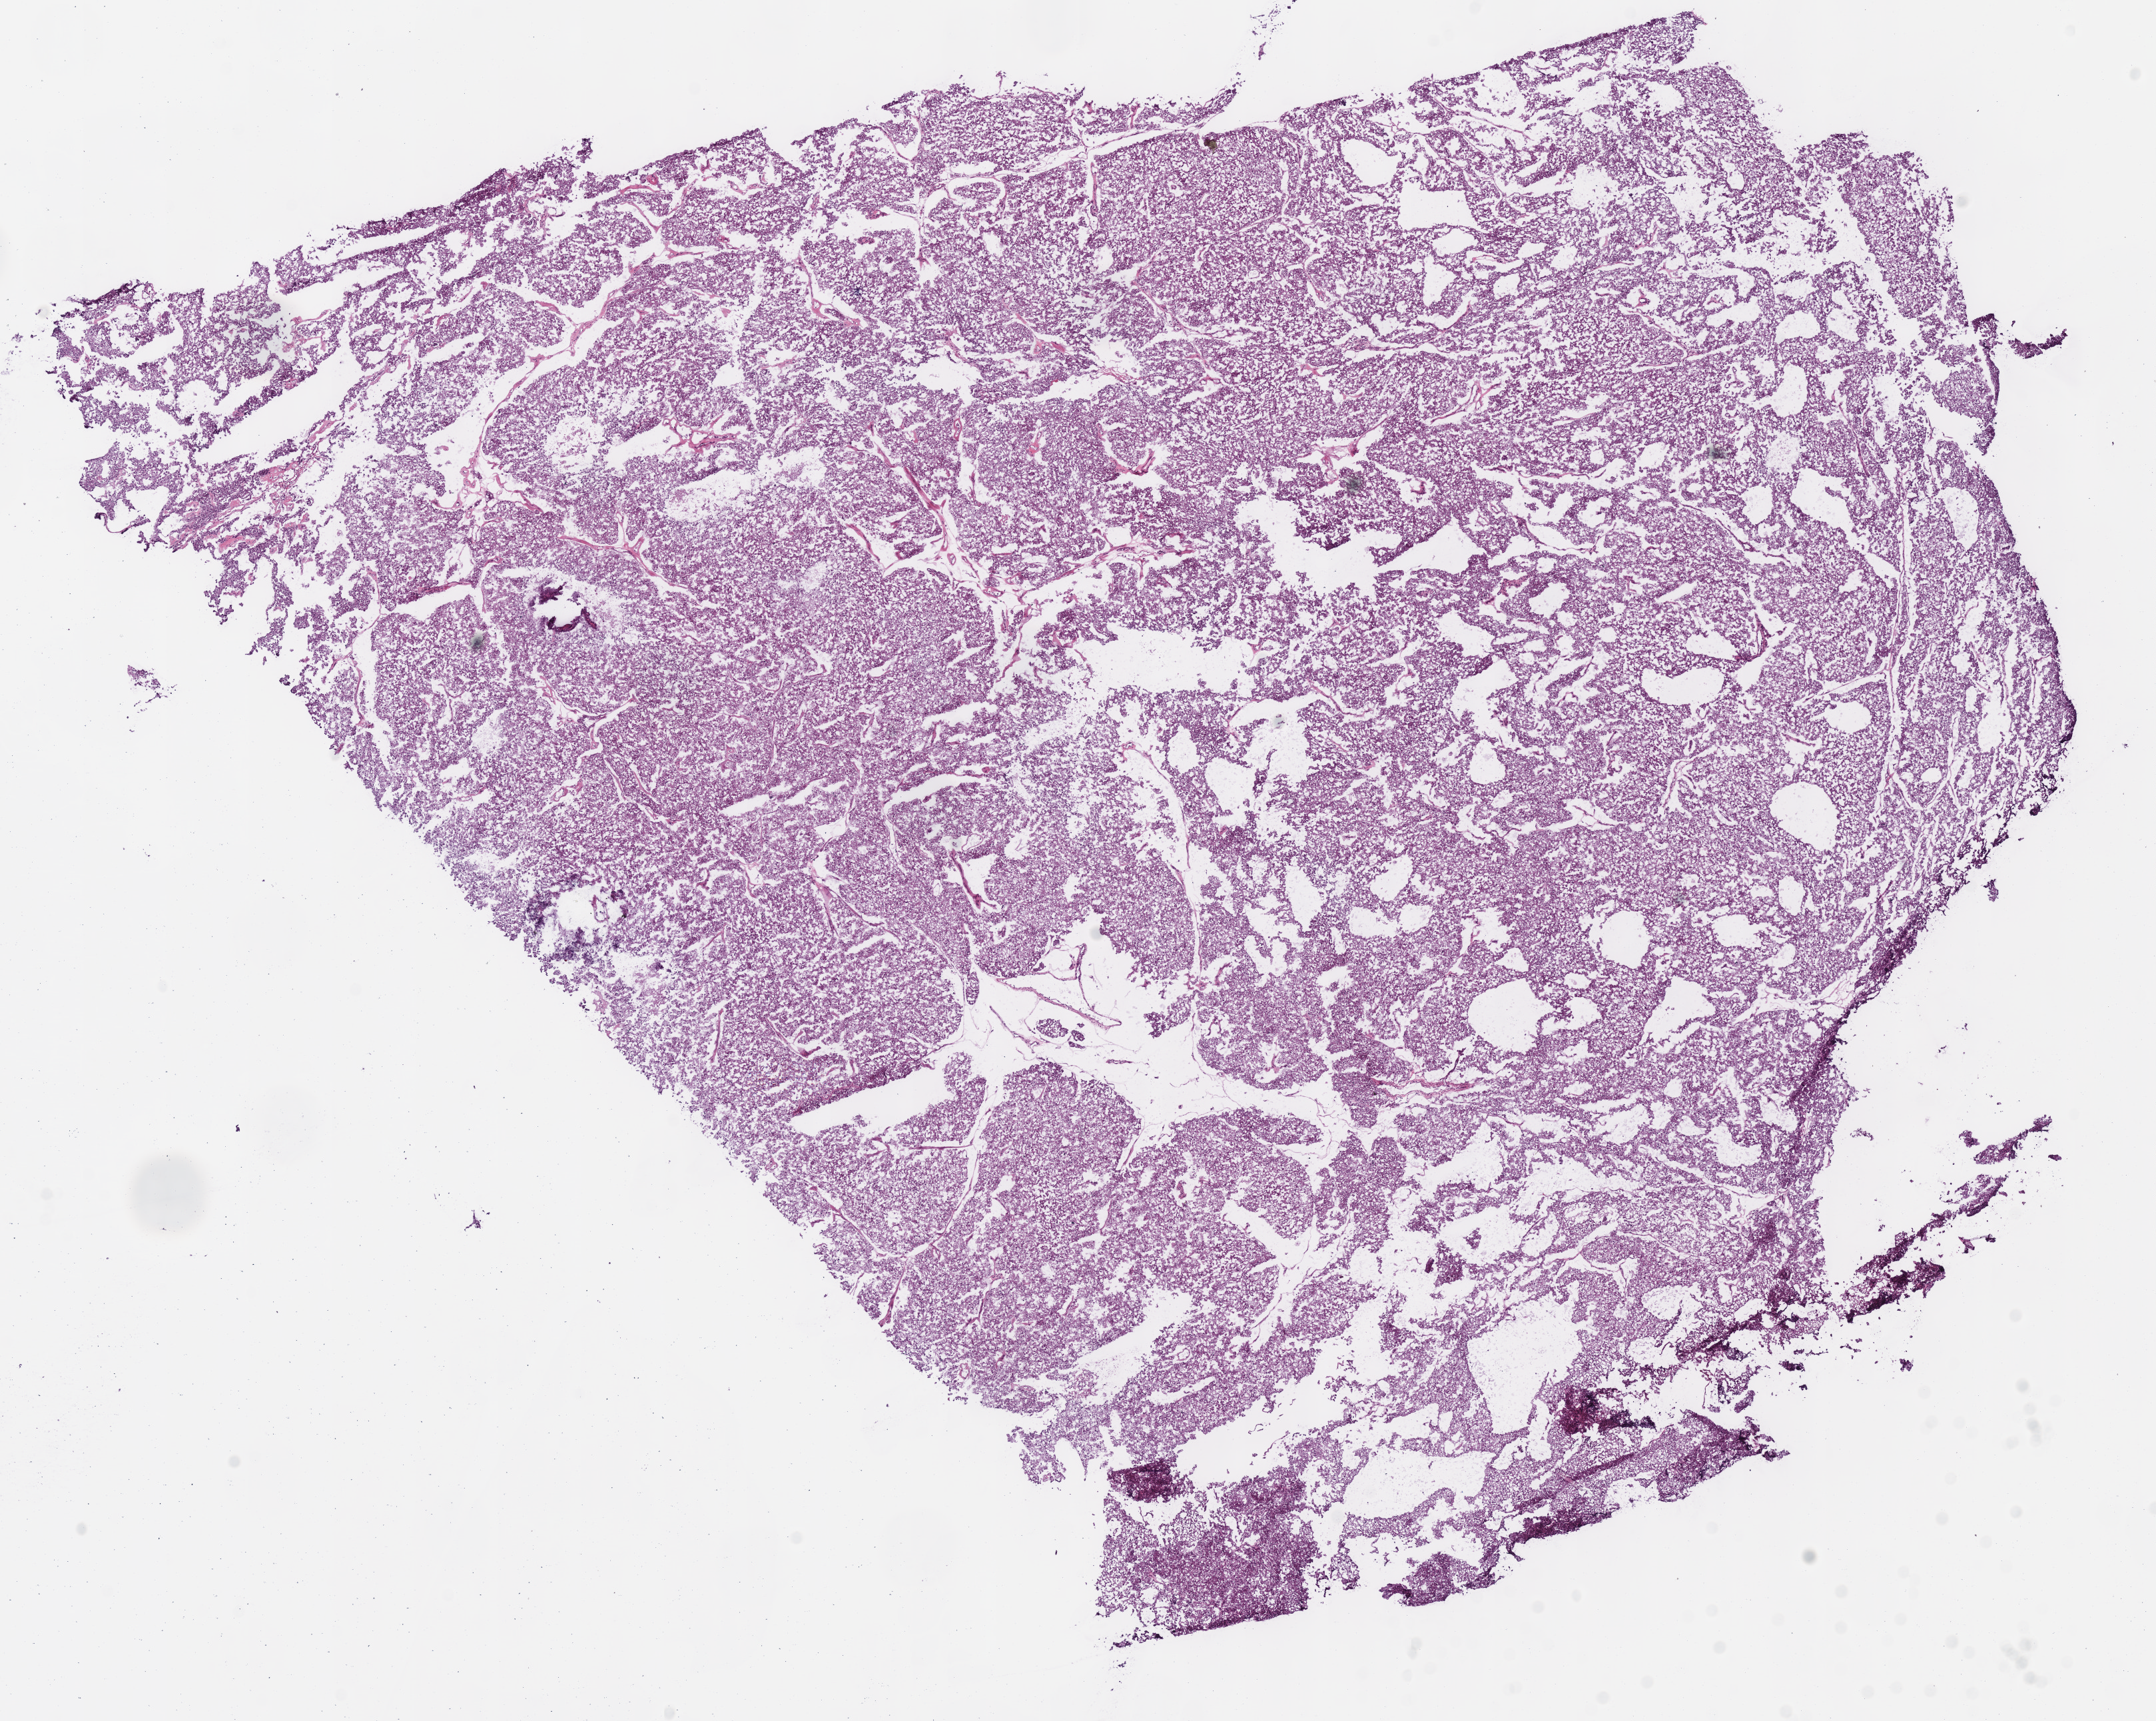
Whole-slide histology image, H&E-stained, a low-resolution overview of the entire scanned area, about 12.7 x 10.2 mm (acquisition: 40x scan), frozen section, sample: primary tumour, kidney. Male, age 62 years at initial diagnosis. Composition of this section per pathologist review: tumour cells 95%, tumour nuclei 90%, normal cells 0%, stromal cells 5%, necrosis 0%.
Lymph nodes positive (case pathology): 0 of 1 examined. Laterality: right. AJCC pathologic stage: II (6th edition). Pathologic diagnosis: Renal cell carcinoma, chromophobe type.